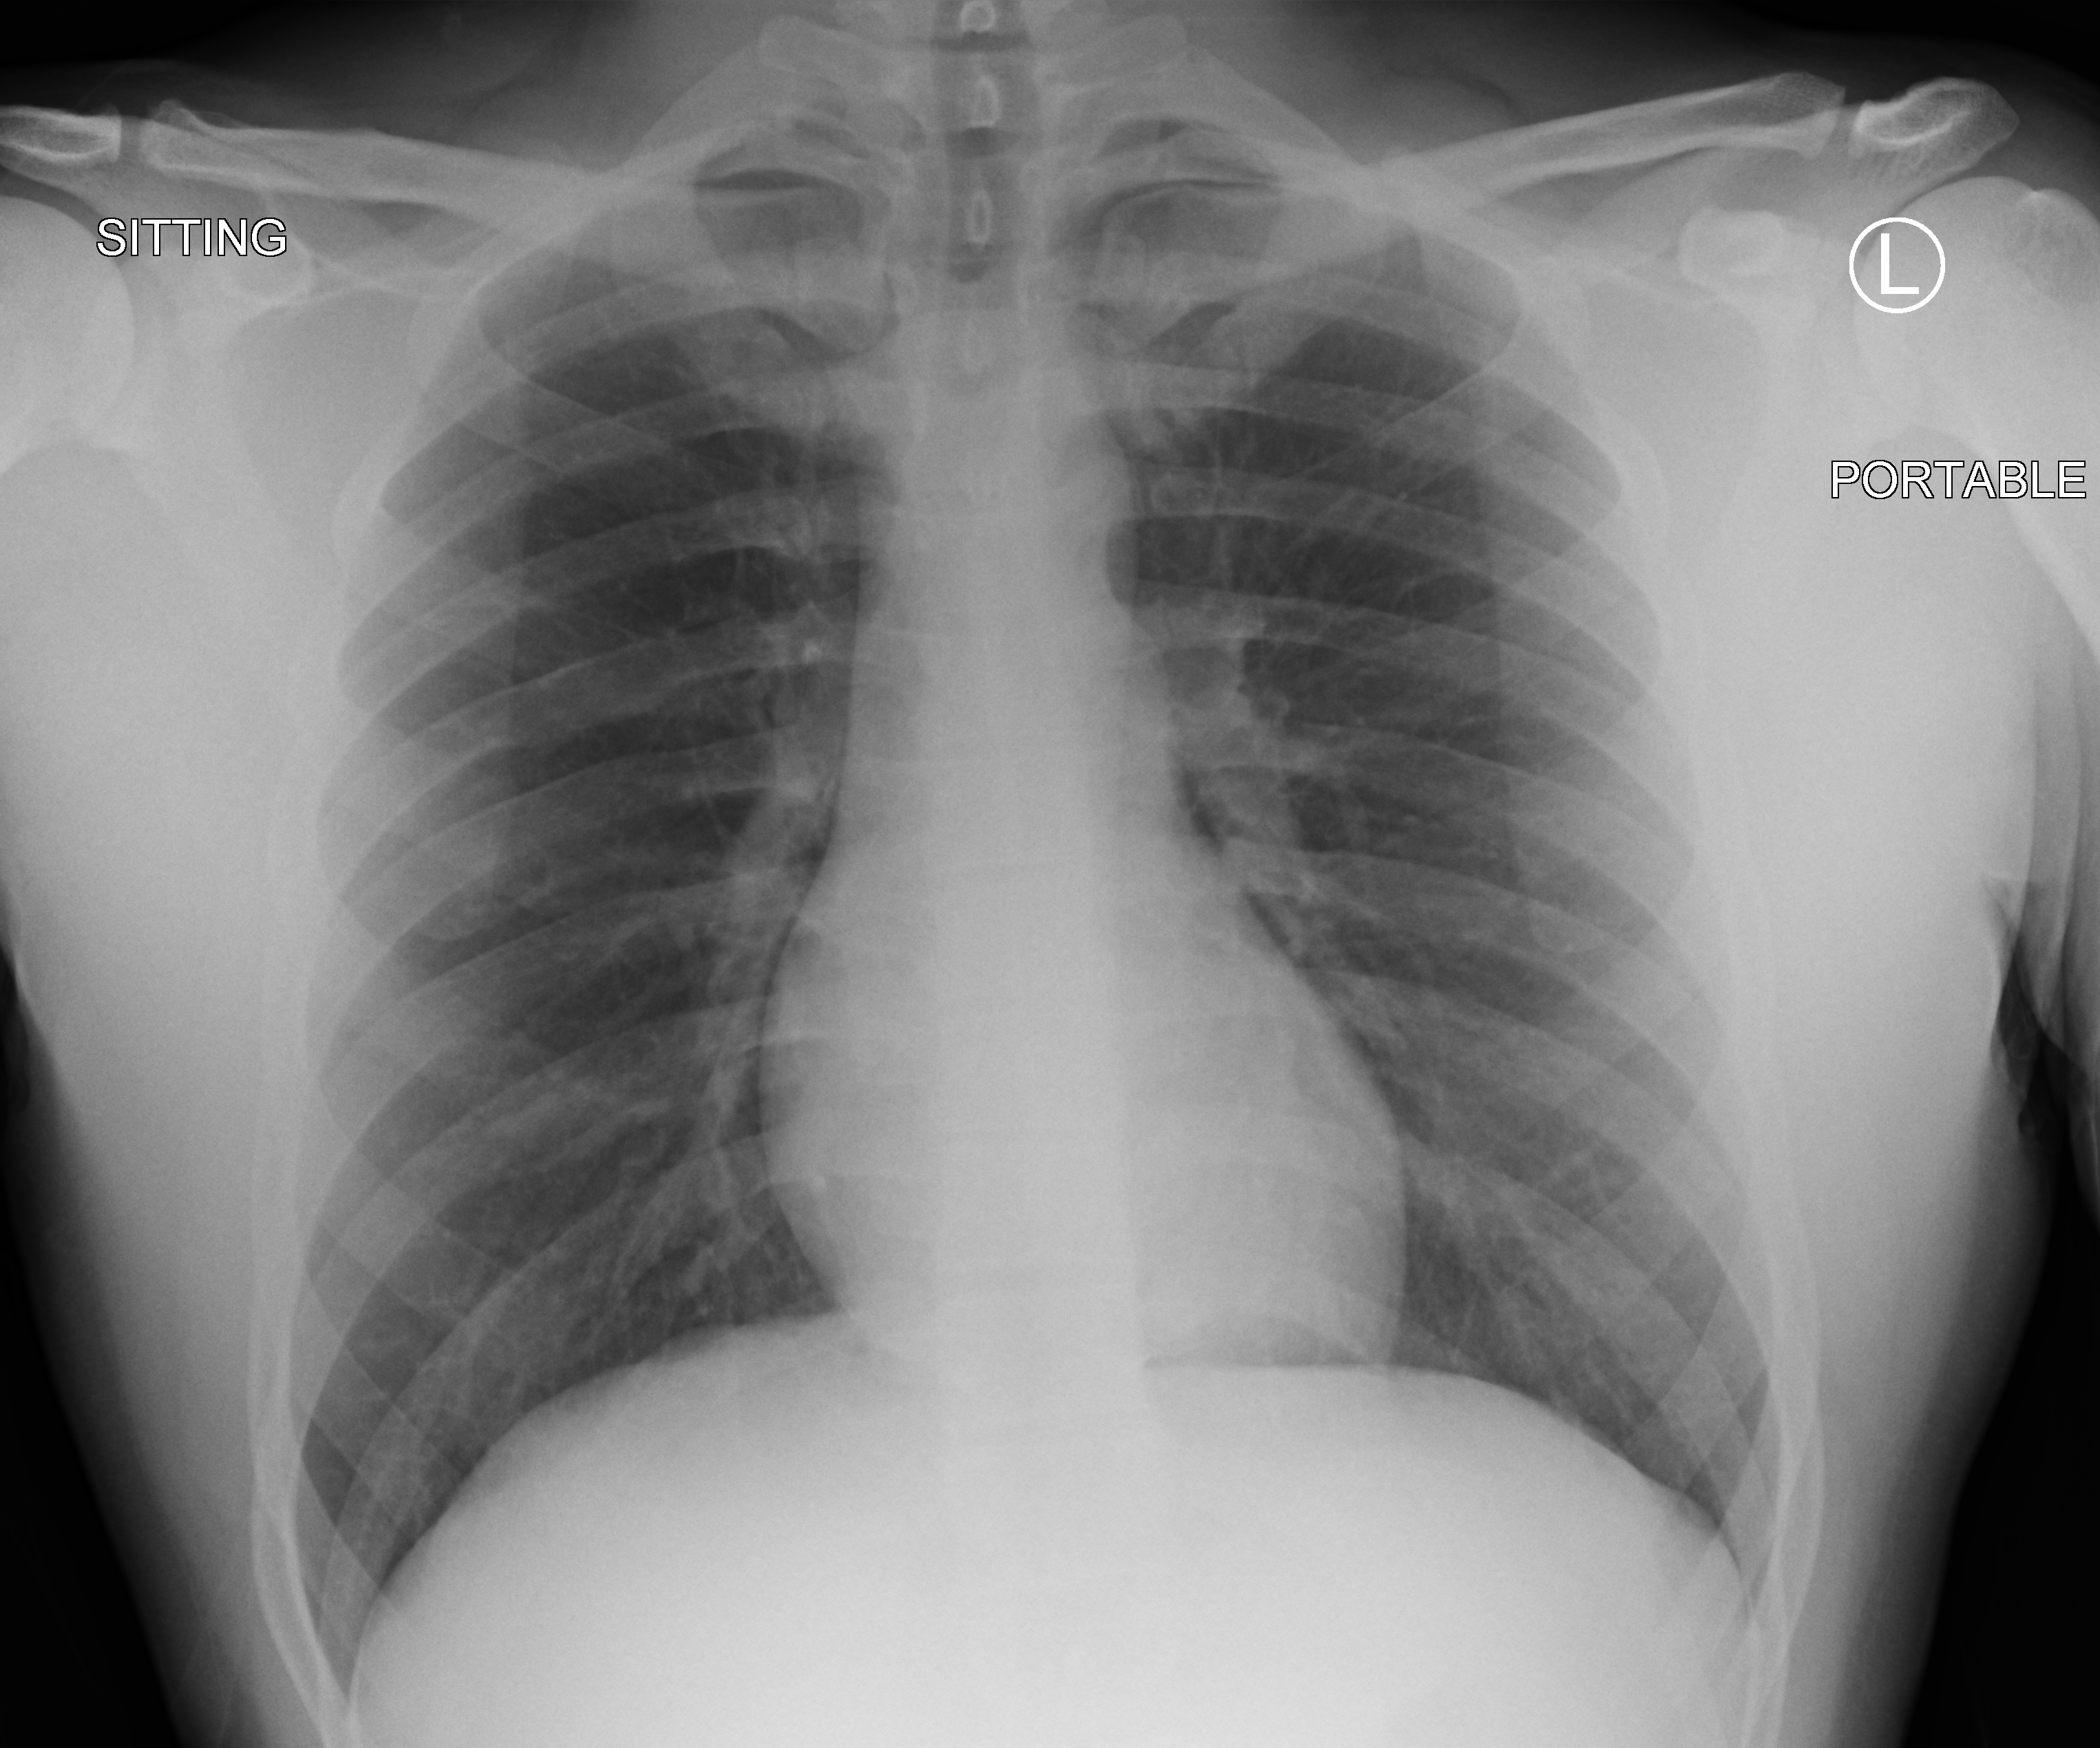
Chest X-ray (portable), anteroposterior (AP) projection. Male patient hospitalised with COVID-19, age 18–59 years.
Hospital-stay facts (about this admission, not read from this image; timing relative to this image not recorded):
- COPD (admission record): no
- length of hospital stay: 1 day